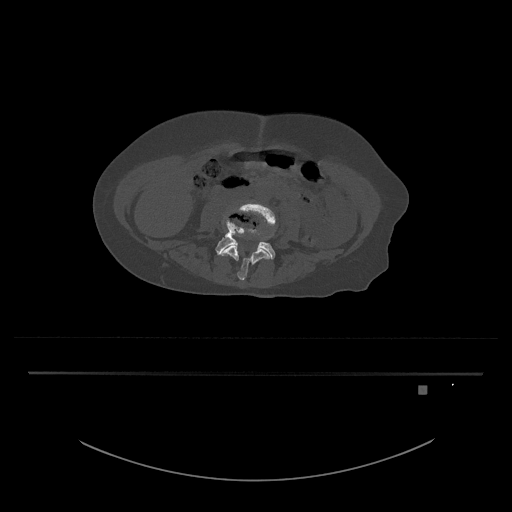
CT including the spine, one axial slice. Position 335 of 797 along the scan axis. Reconstruction kernel Br40s/3. Bone window (W 1800 / L 400 HU). 512 × 512 image matrix. Patient: female, 57 years. From the clinical record (not read from this slice): primary cancer: cervical.
Outlined on this slice (semi-automatically segmented with operator editing):
- L4 vertebra: bounding box [x1, y1, x2, y2] px = [220, 201, 276, 281]